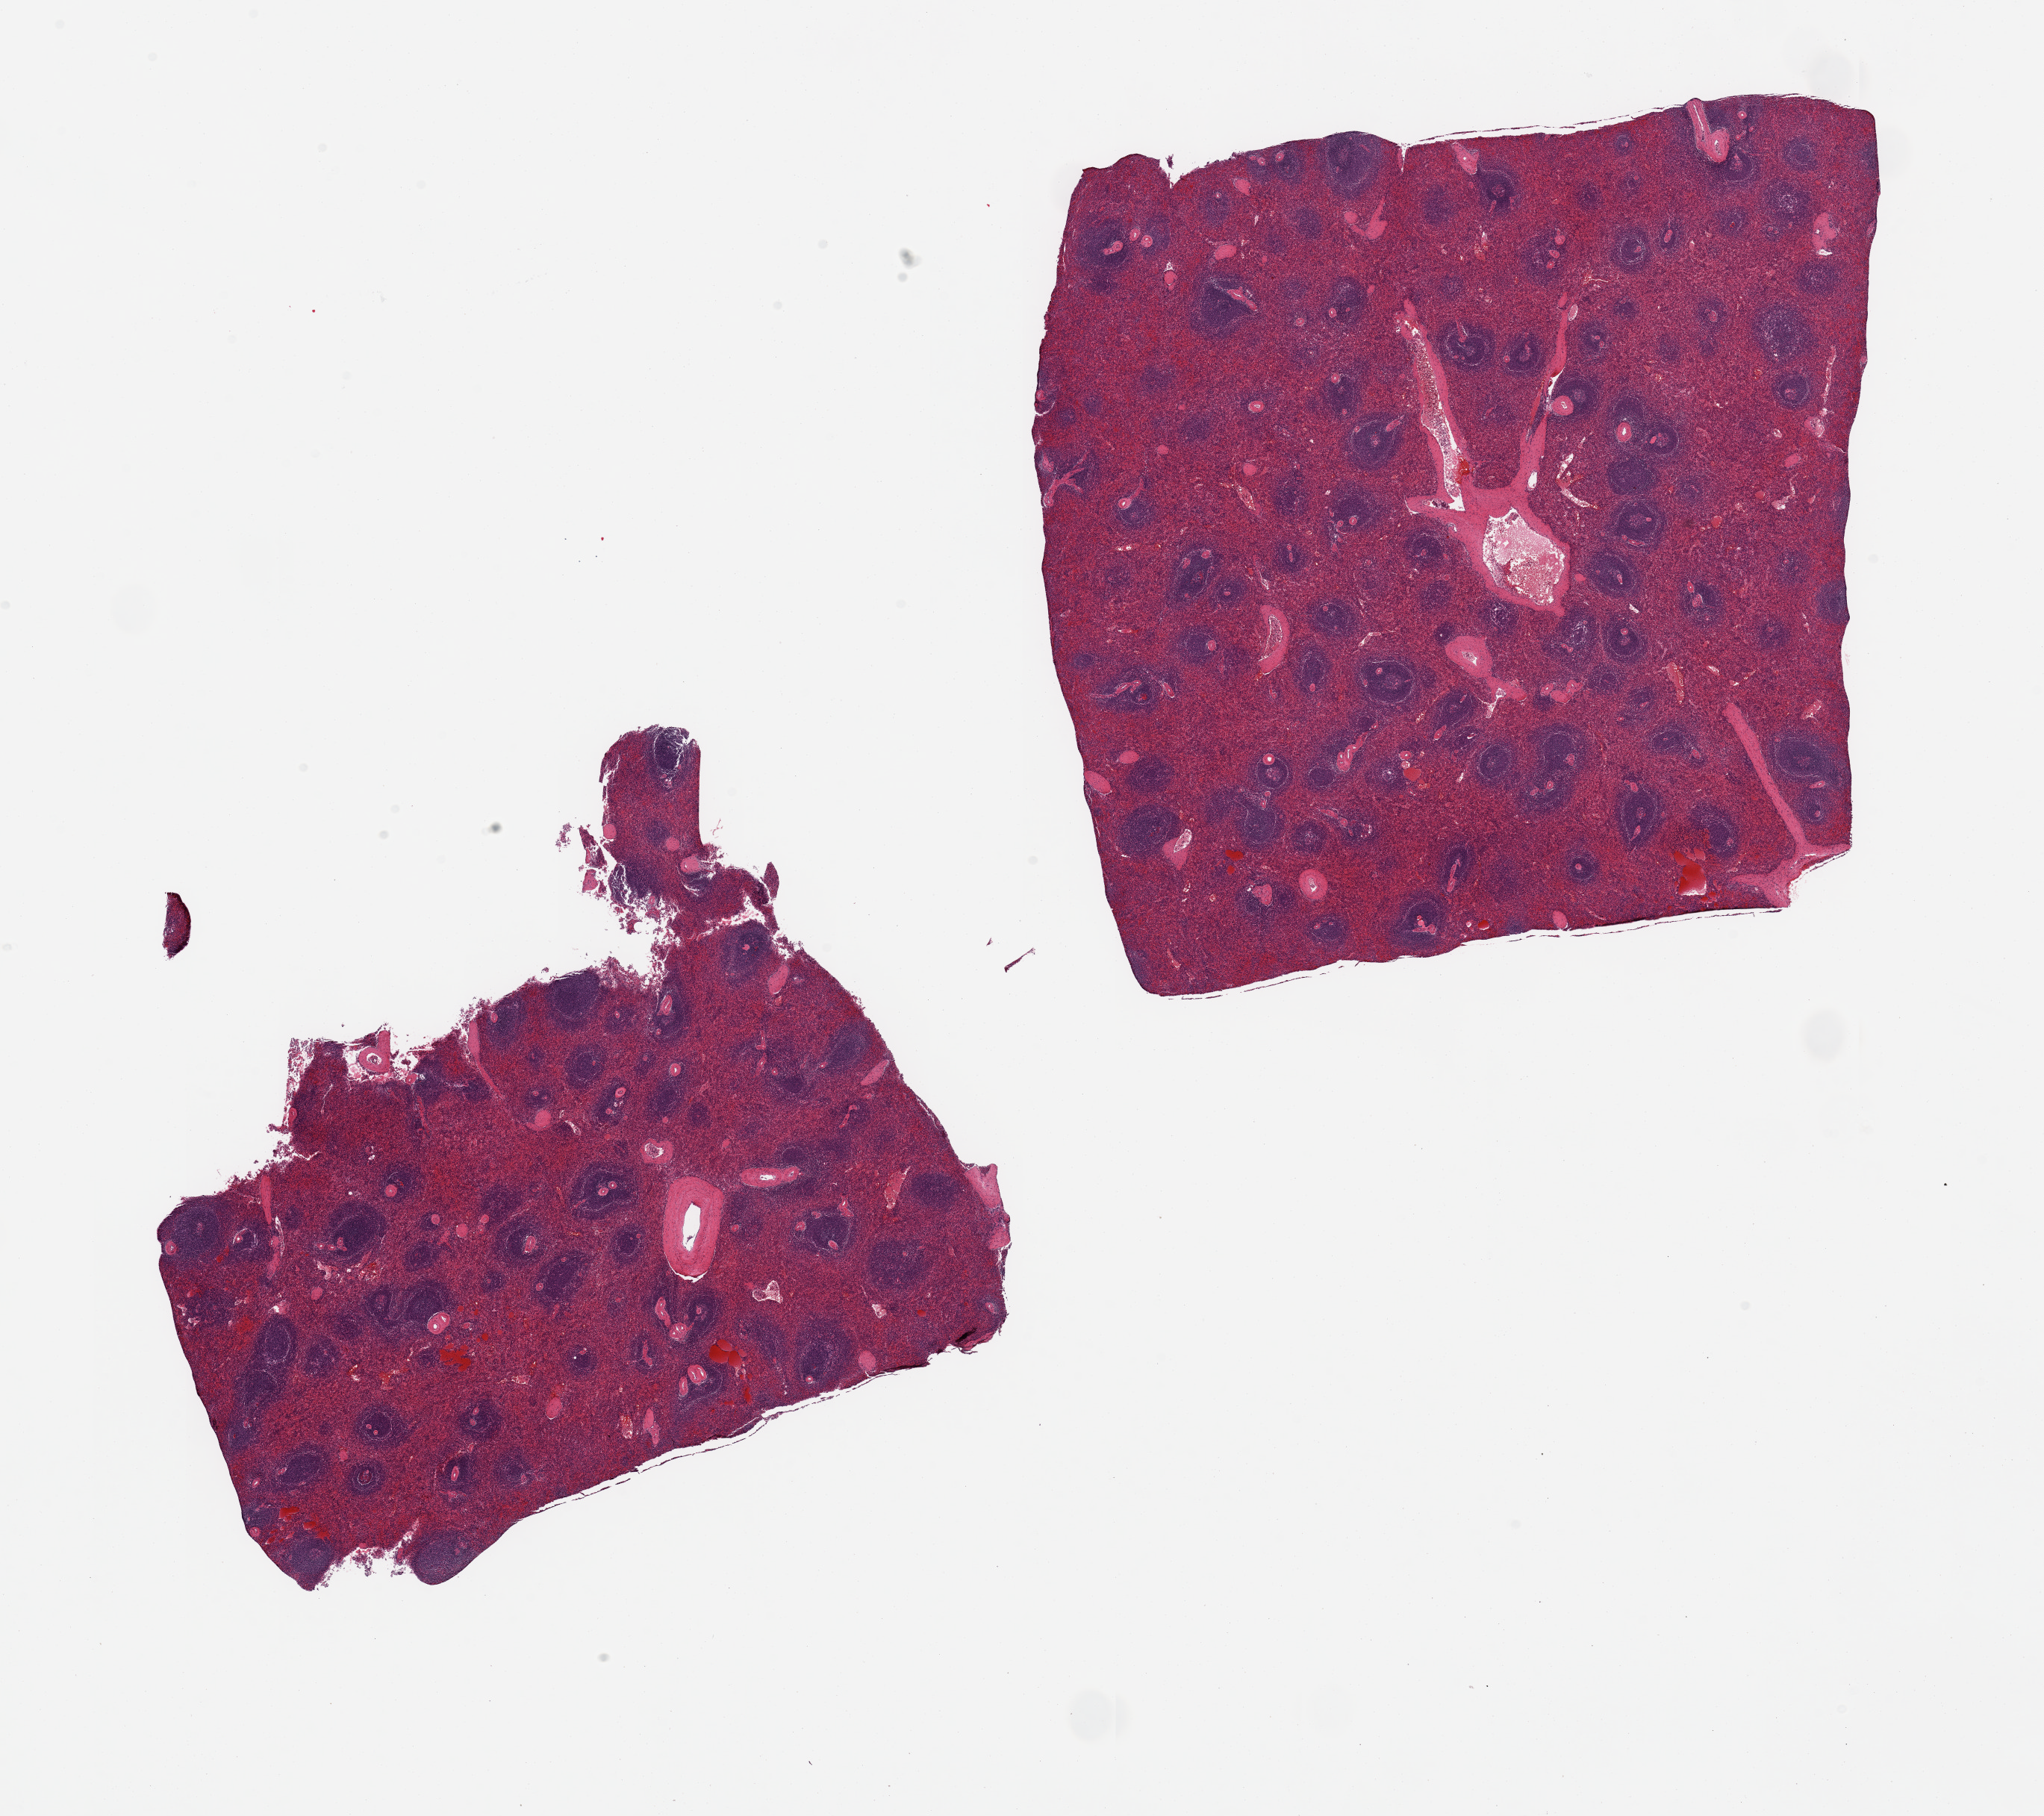
Whole-slide image, H&E stain, brightfield — shown as a low-resolution overview of the whole scanned area (about 21.7 x 19.2 mm, acquisition: 20x scan); PAXgene-fixed paraffin-embedded (PFPE) section; section of spleen (target tissue); donor tissue sample. Donor: female.
Pathologist's review note for this sample: 2 pieces, no abnormalities.